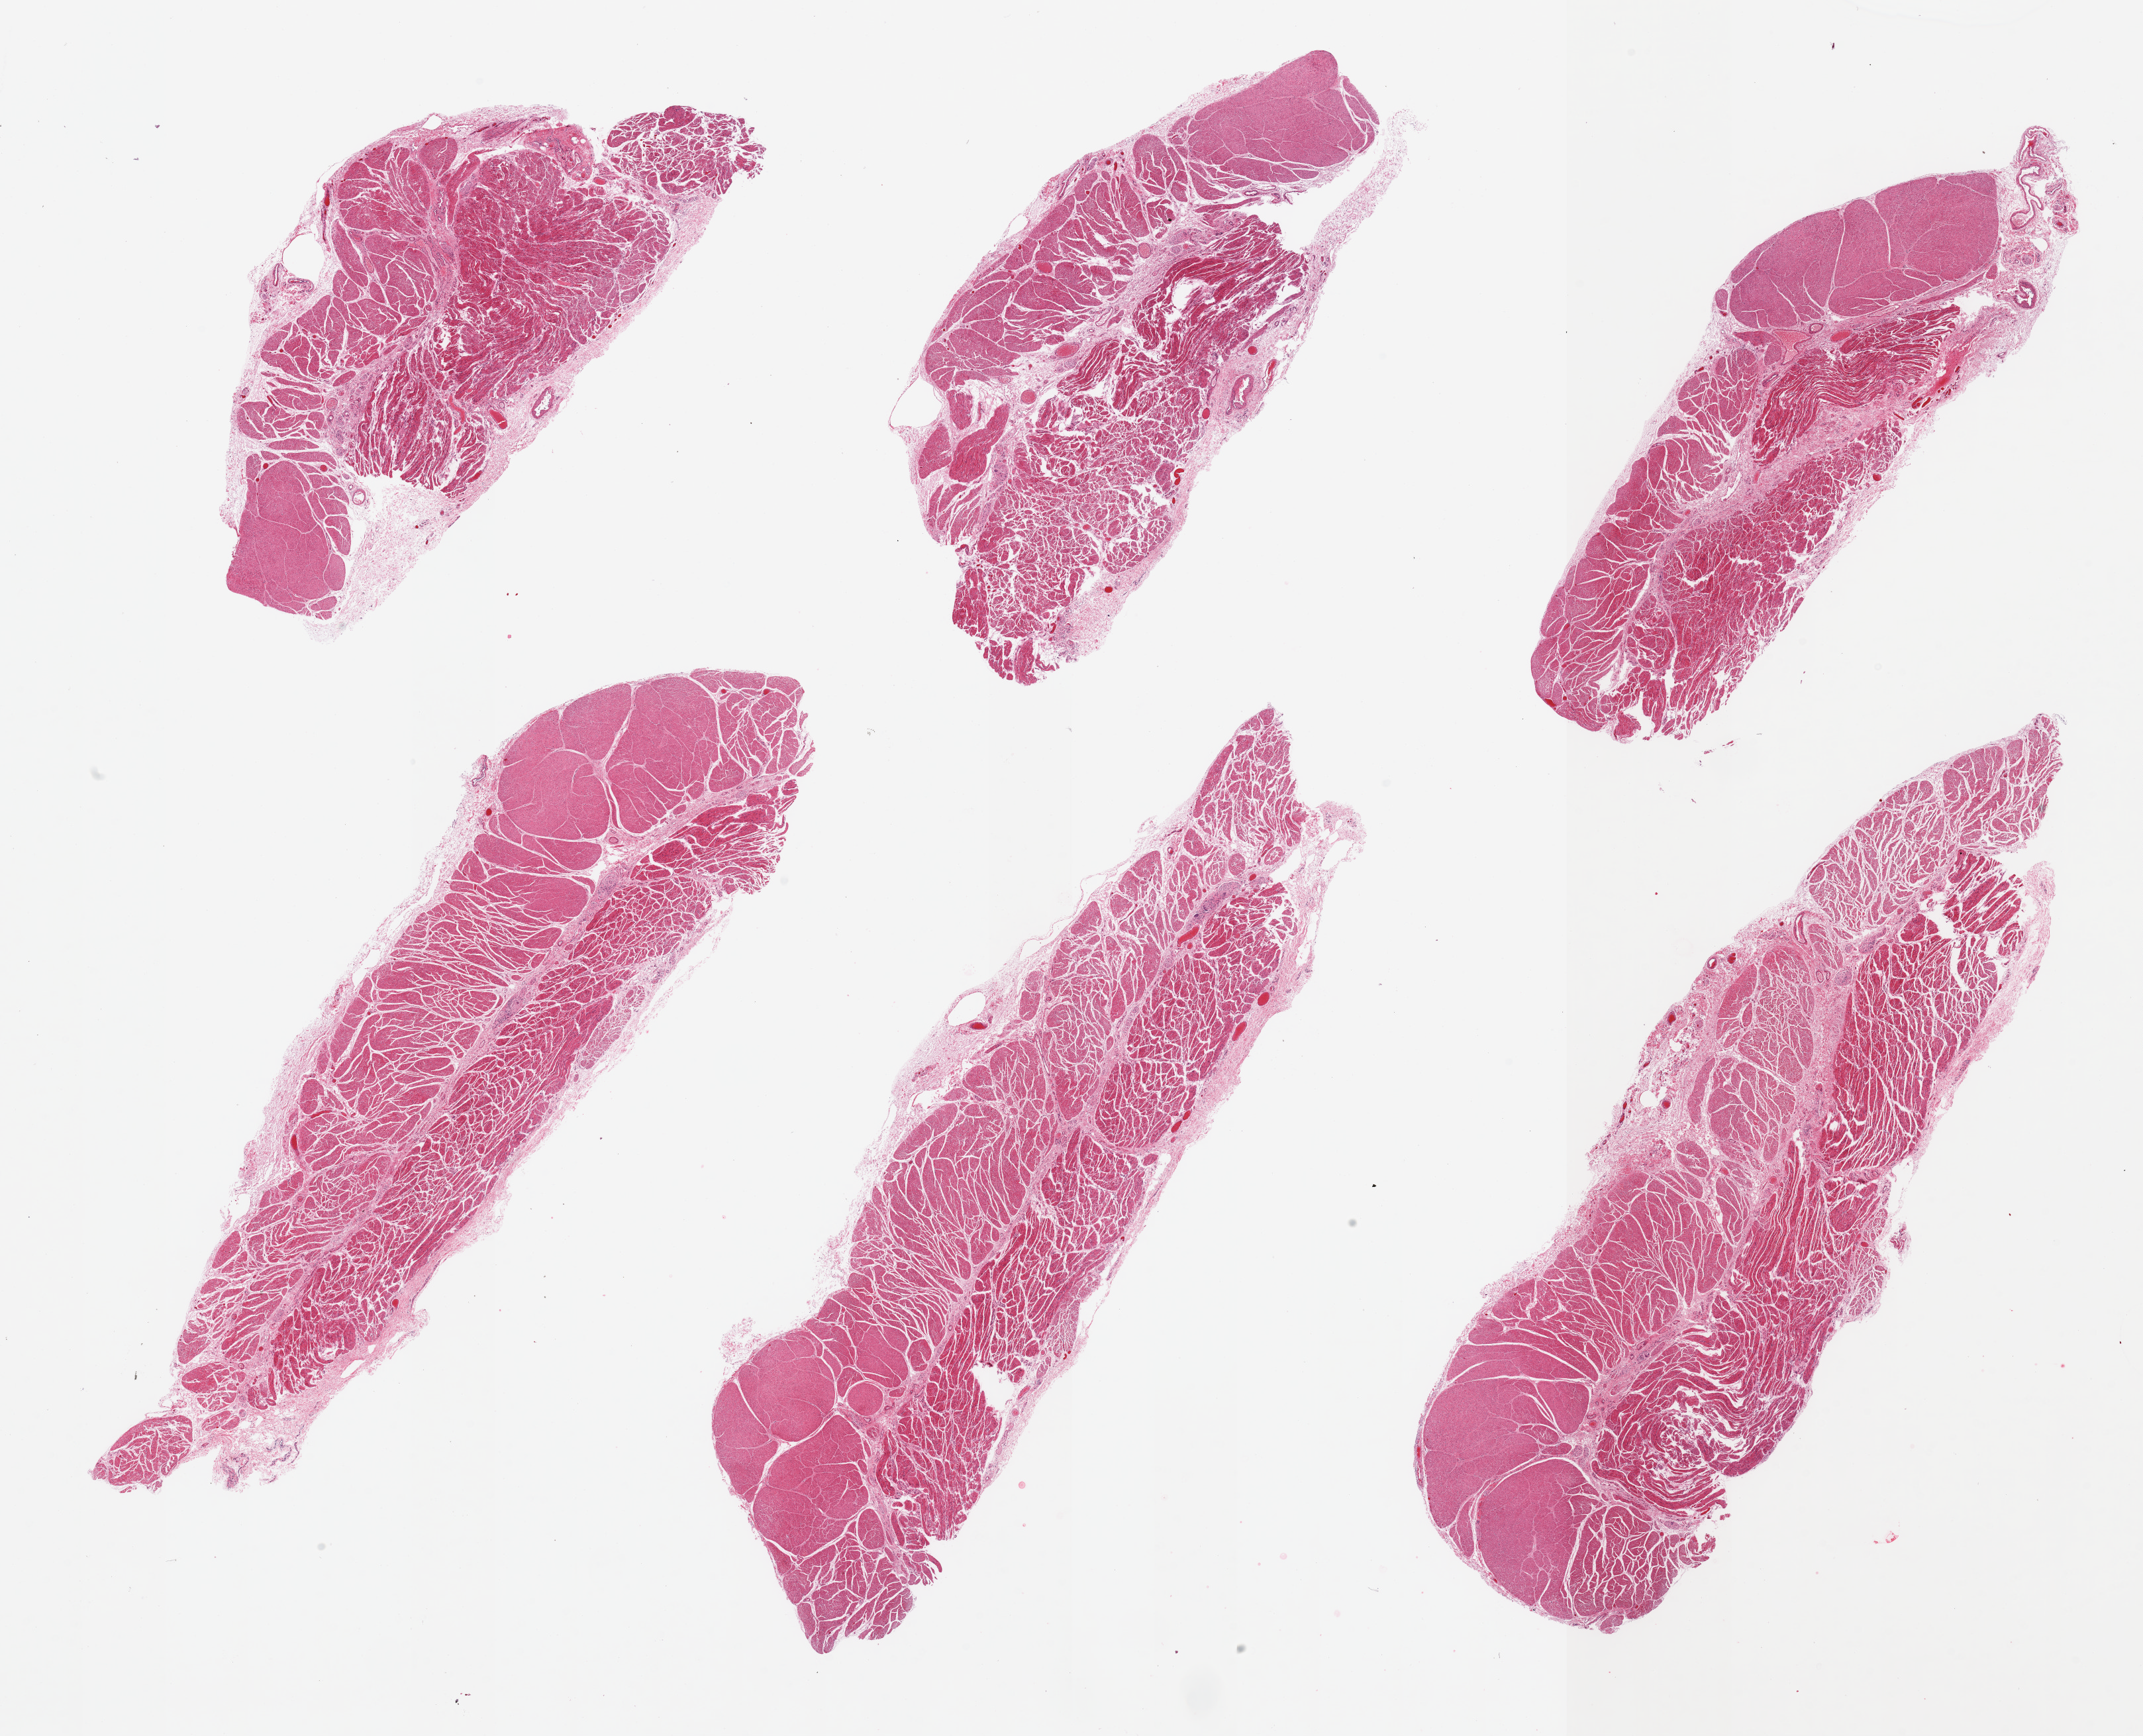
Whole-slide image, haematoxylin and eosin stain, low-resolution overview of the scanned area, about 25.6 x 20.7 mm; PAXgene-fixed, paraffin-embedded tissue; target tissue: esophageal muscle; tissue donor sample. Male donor.
Reviewer comment on this tissue sample: 6 pieces, confirmed target muscularis.